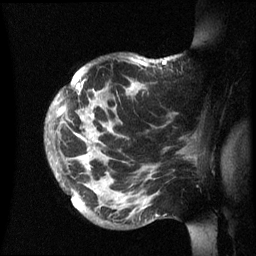
Breast MRI (dynamic contrast-enhanced), one sagittal slice. Slice 45 of 60 in the series (ordered by position). Dynamic contrast-enhanced series, image 2 of 3 at this slice position (ordered by acquisition). 1.5 T. TE 4.2 ms, TR 8.4 ms. 2.4 mm slice thickness. 256 × 256 image matrix, field of view 230 × 230 mm. Patient: female, 48 years.
Structures marked on this image (semi-automatically segmented with operator editing):
- analysis volume of interest (the breast-tissue region the enhancement analysis was run in; not a lesion): bounding box [x1, y1, x2, y2] px = [47, 56, 202, 236]
- tumour enhancement mask (voxels above the 70 % enhancement threshold inside the analysis volume of interest): [55, 59, 167, 168]